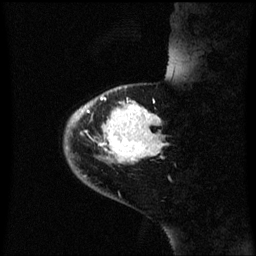
Breast MRI (dynamic contrast-enhanced), one sagittal slice. Slice 14 of 60 in the series (ordered by position). Dynamic contrast-enhanced series, image 2 of 3 at this slice position (ordered by acquisition). 1.5 T. TE 4.2 ms, TR 8.4 ms. 256 × 256 image matrix, field of view 200 × 200 mm. Female patient, age 46 years. Case-level facts recorded for this patient, not image findings: setting: breast cancer imaged before/during neoadjuvant chemotherapy; receptor status: HER2-positive.
Outlined on this slice (semi-automatic segmentation, software-assisted and operator-edited):
- analysis volume of interest (the breast-tissue region the enhancement analysis was run in; not a lesion): bounding box (x1, y1, x2, y2) in pixels: (64, 86, 167, 171)
- tumour enhancement mask (voxels above the 70 % enhancement threshold inside the analysis volume of interest): (74, 102, 163, 163)